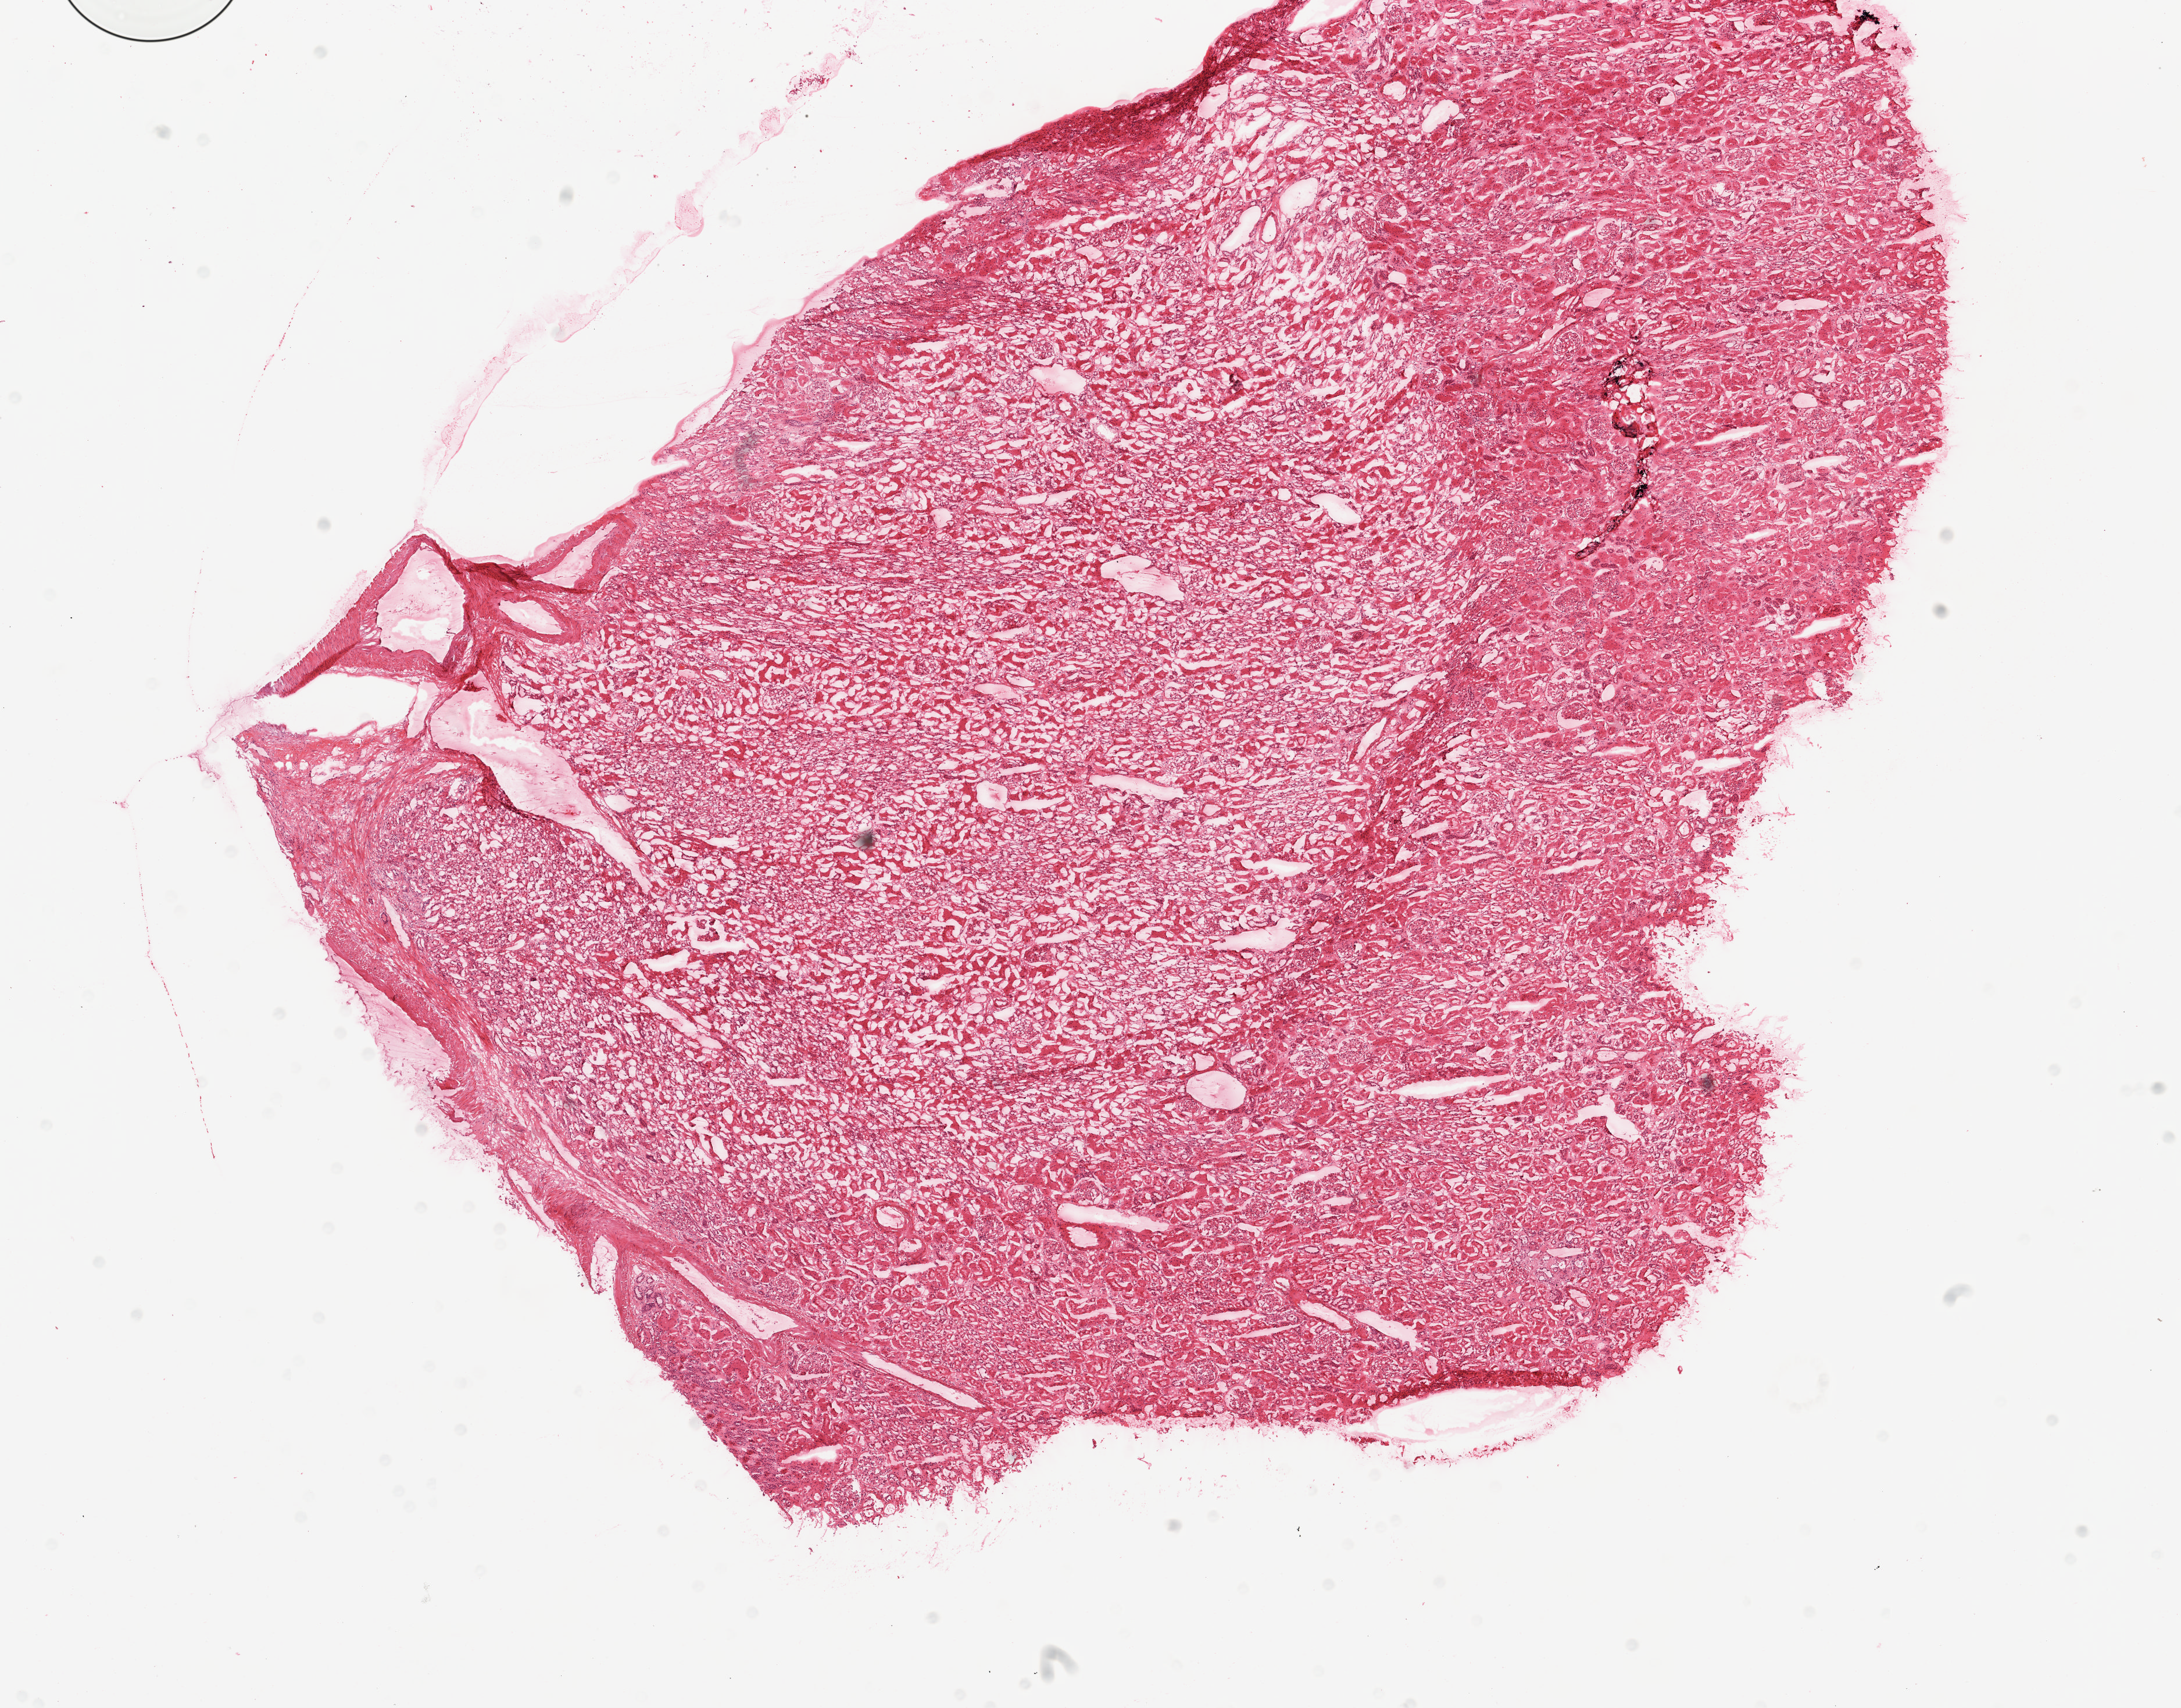
H&E-stained whole-slide image — whole scanned area (about 14.9 x 11.7 mm) shown as a low-resolution overview. Frozen section. Solid tissue normal (non-tumour tissue) sample from the kidney. Patient: female, age at initial diagnosis 66 years.
This section: solid tissue normal (non-tumour) sample from the same patient. Patient diagnosis: Clear cell adenocarcinoma, NOS.